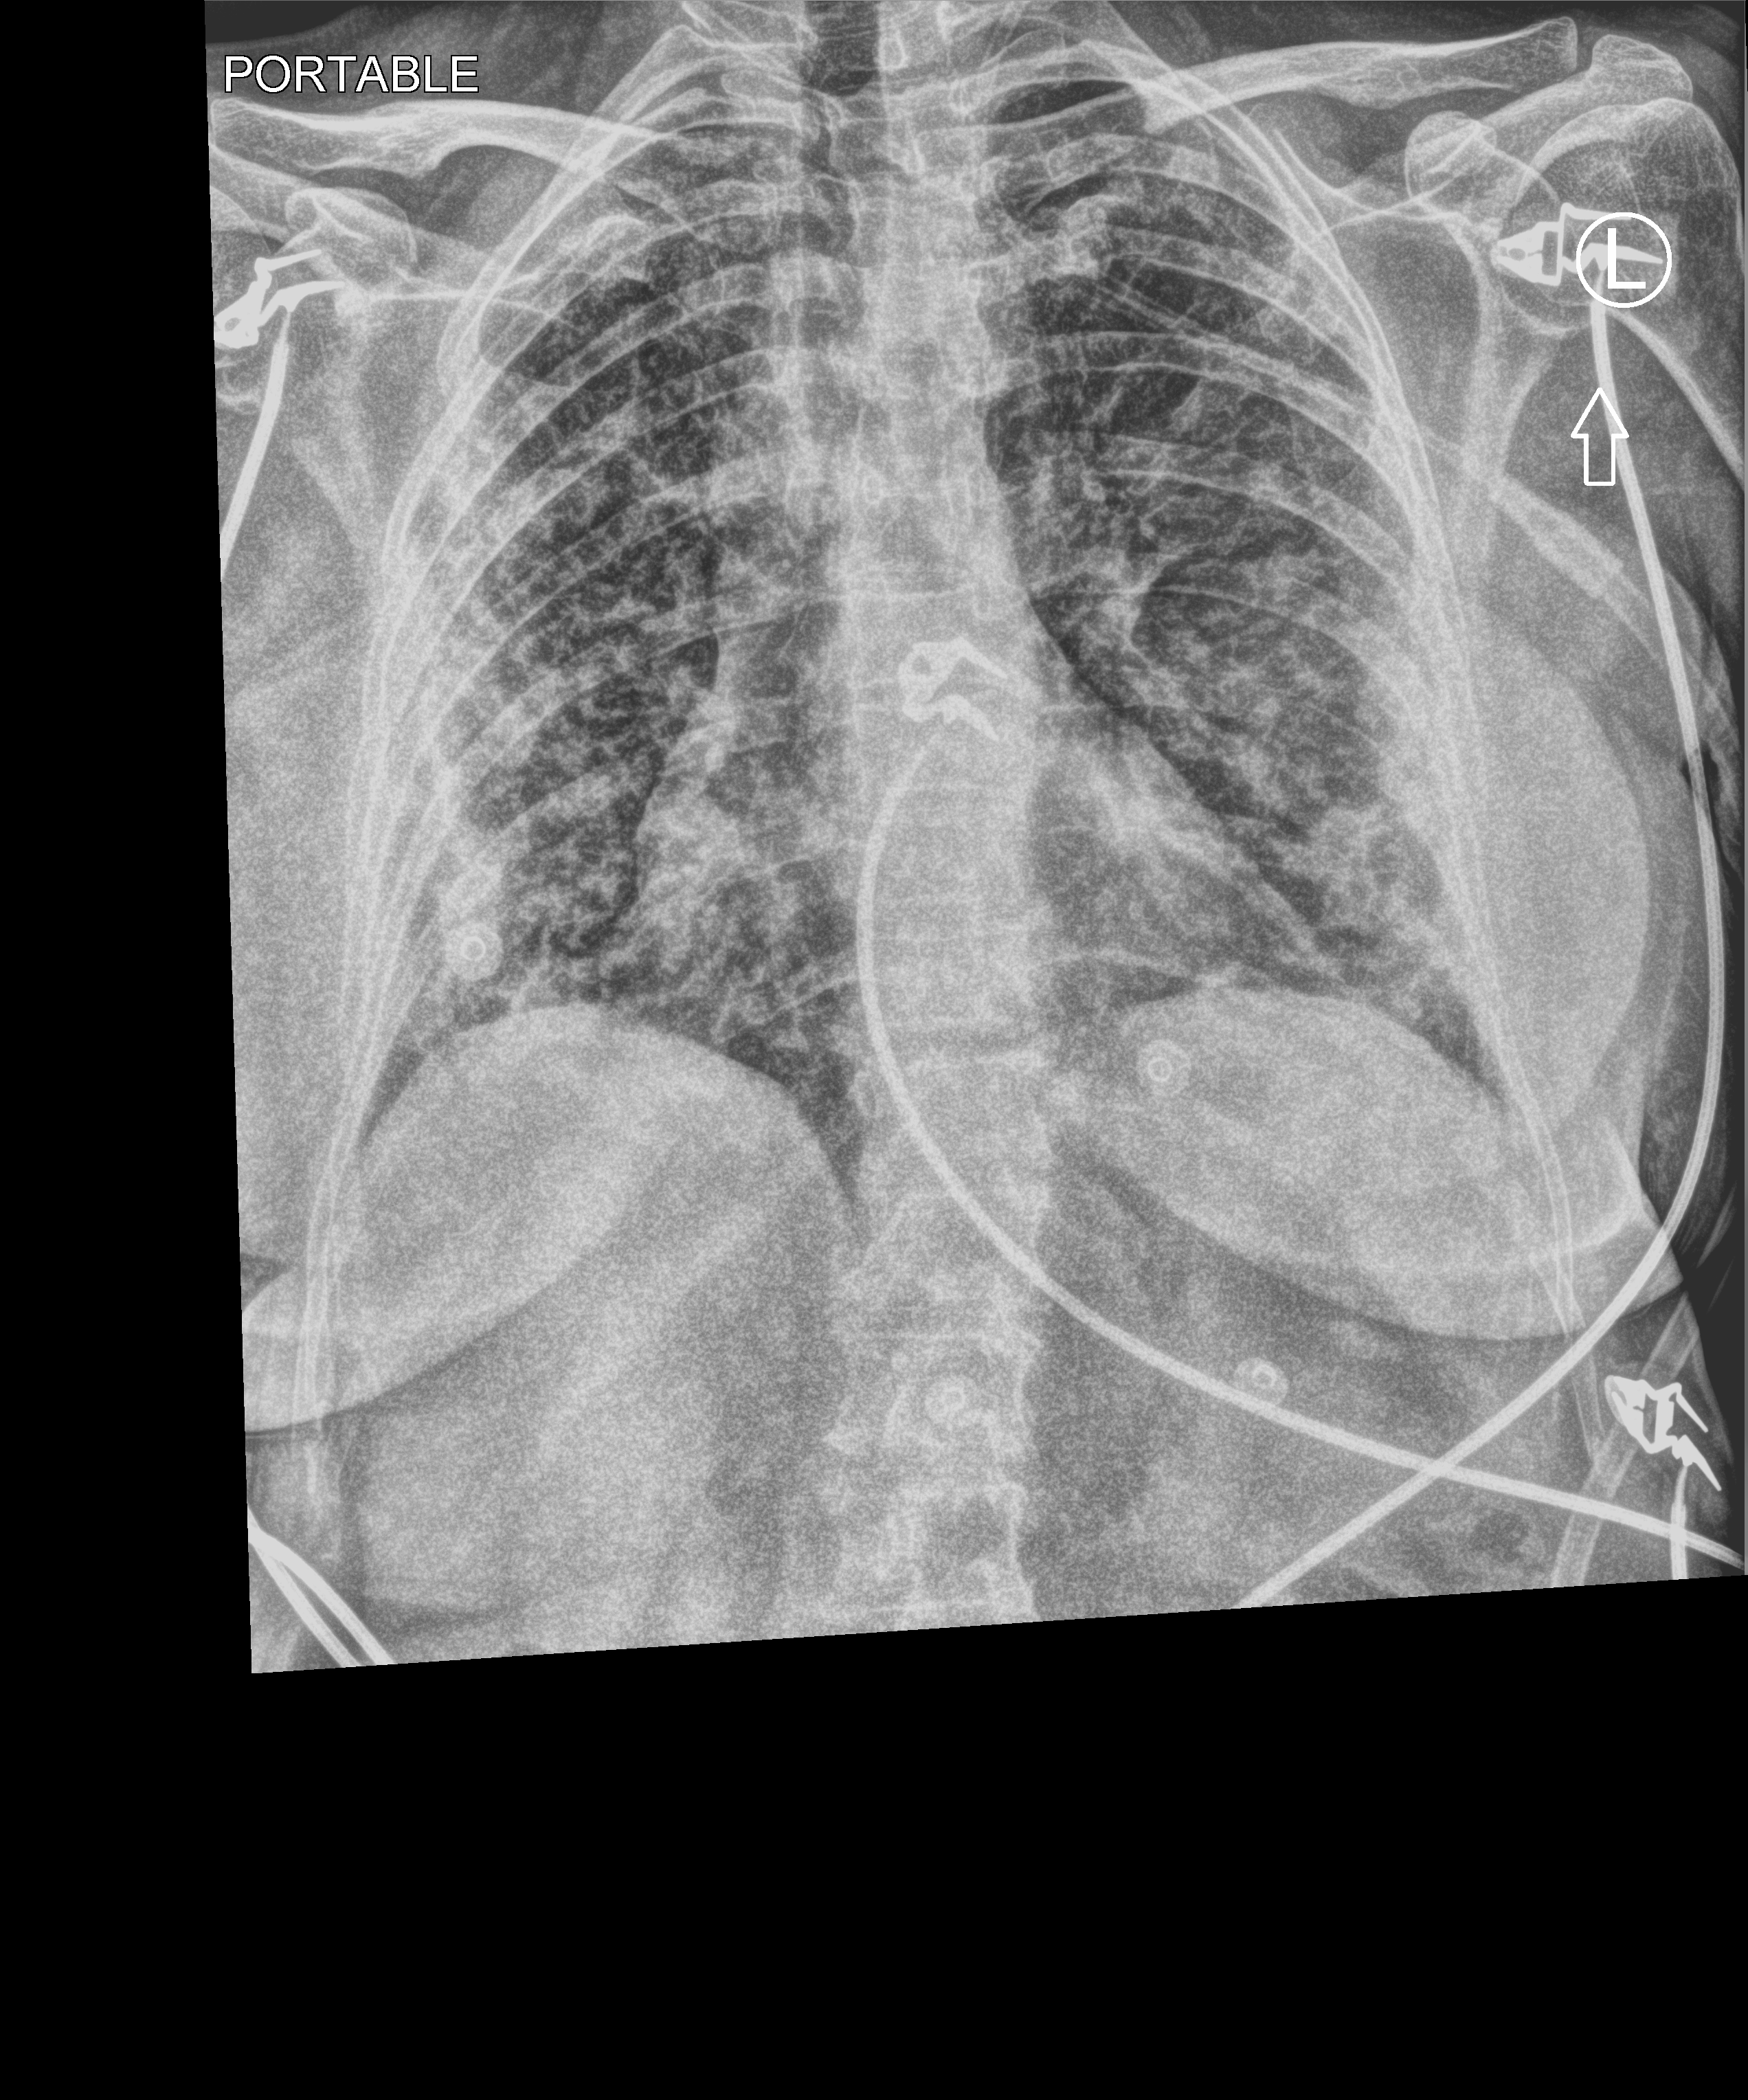
Bedside chest radiograph (computed radiography); anteroposterior (AP) projection. Patient hospitalised with COVID-19; female, aged 60–74 years.
Hospital-stay facts (about this admission, not read from this image; timing relative to this image not recorded):
- admitted to intensive care during this hospital stay: no